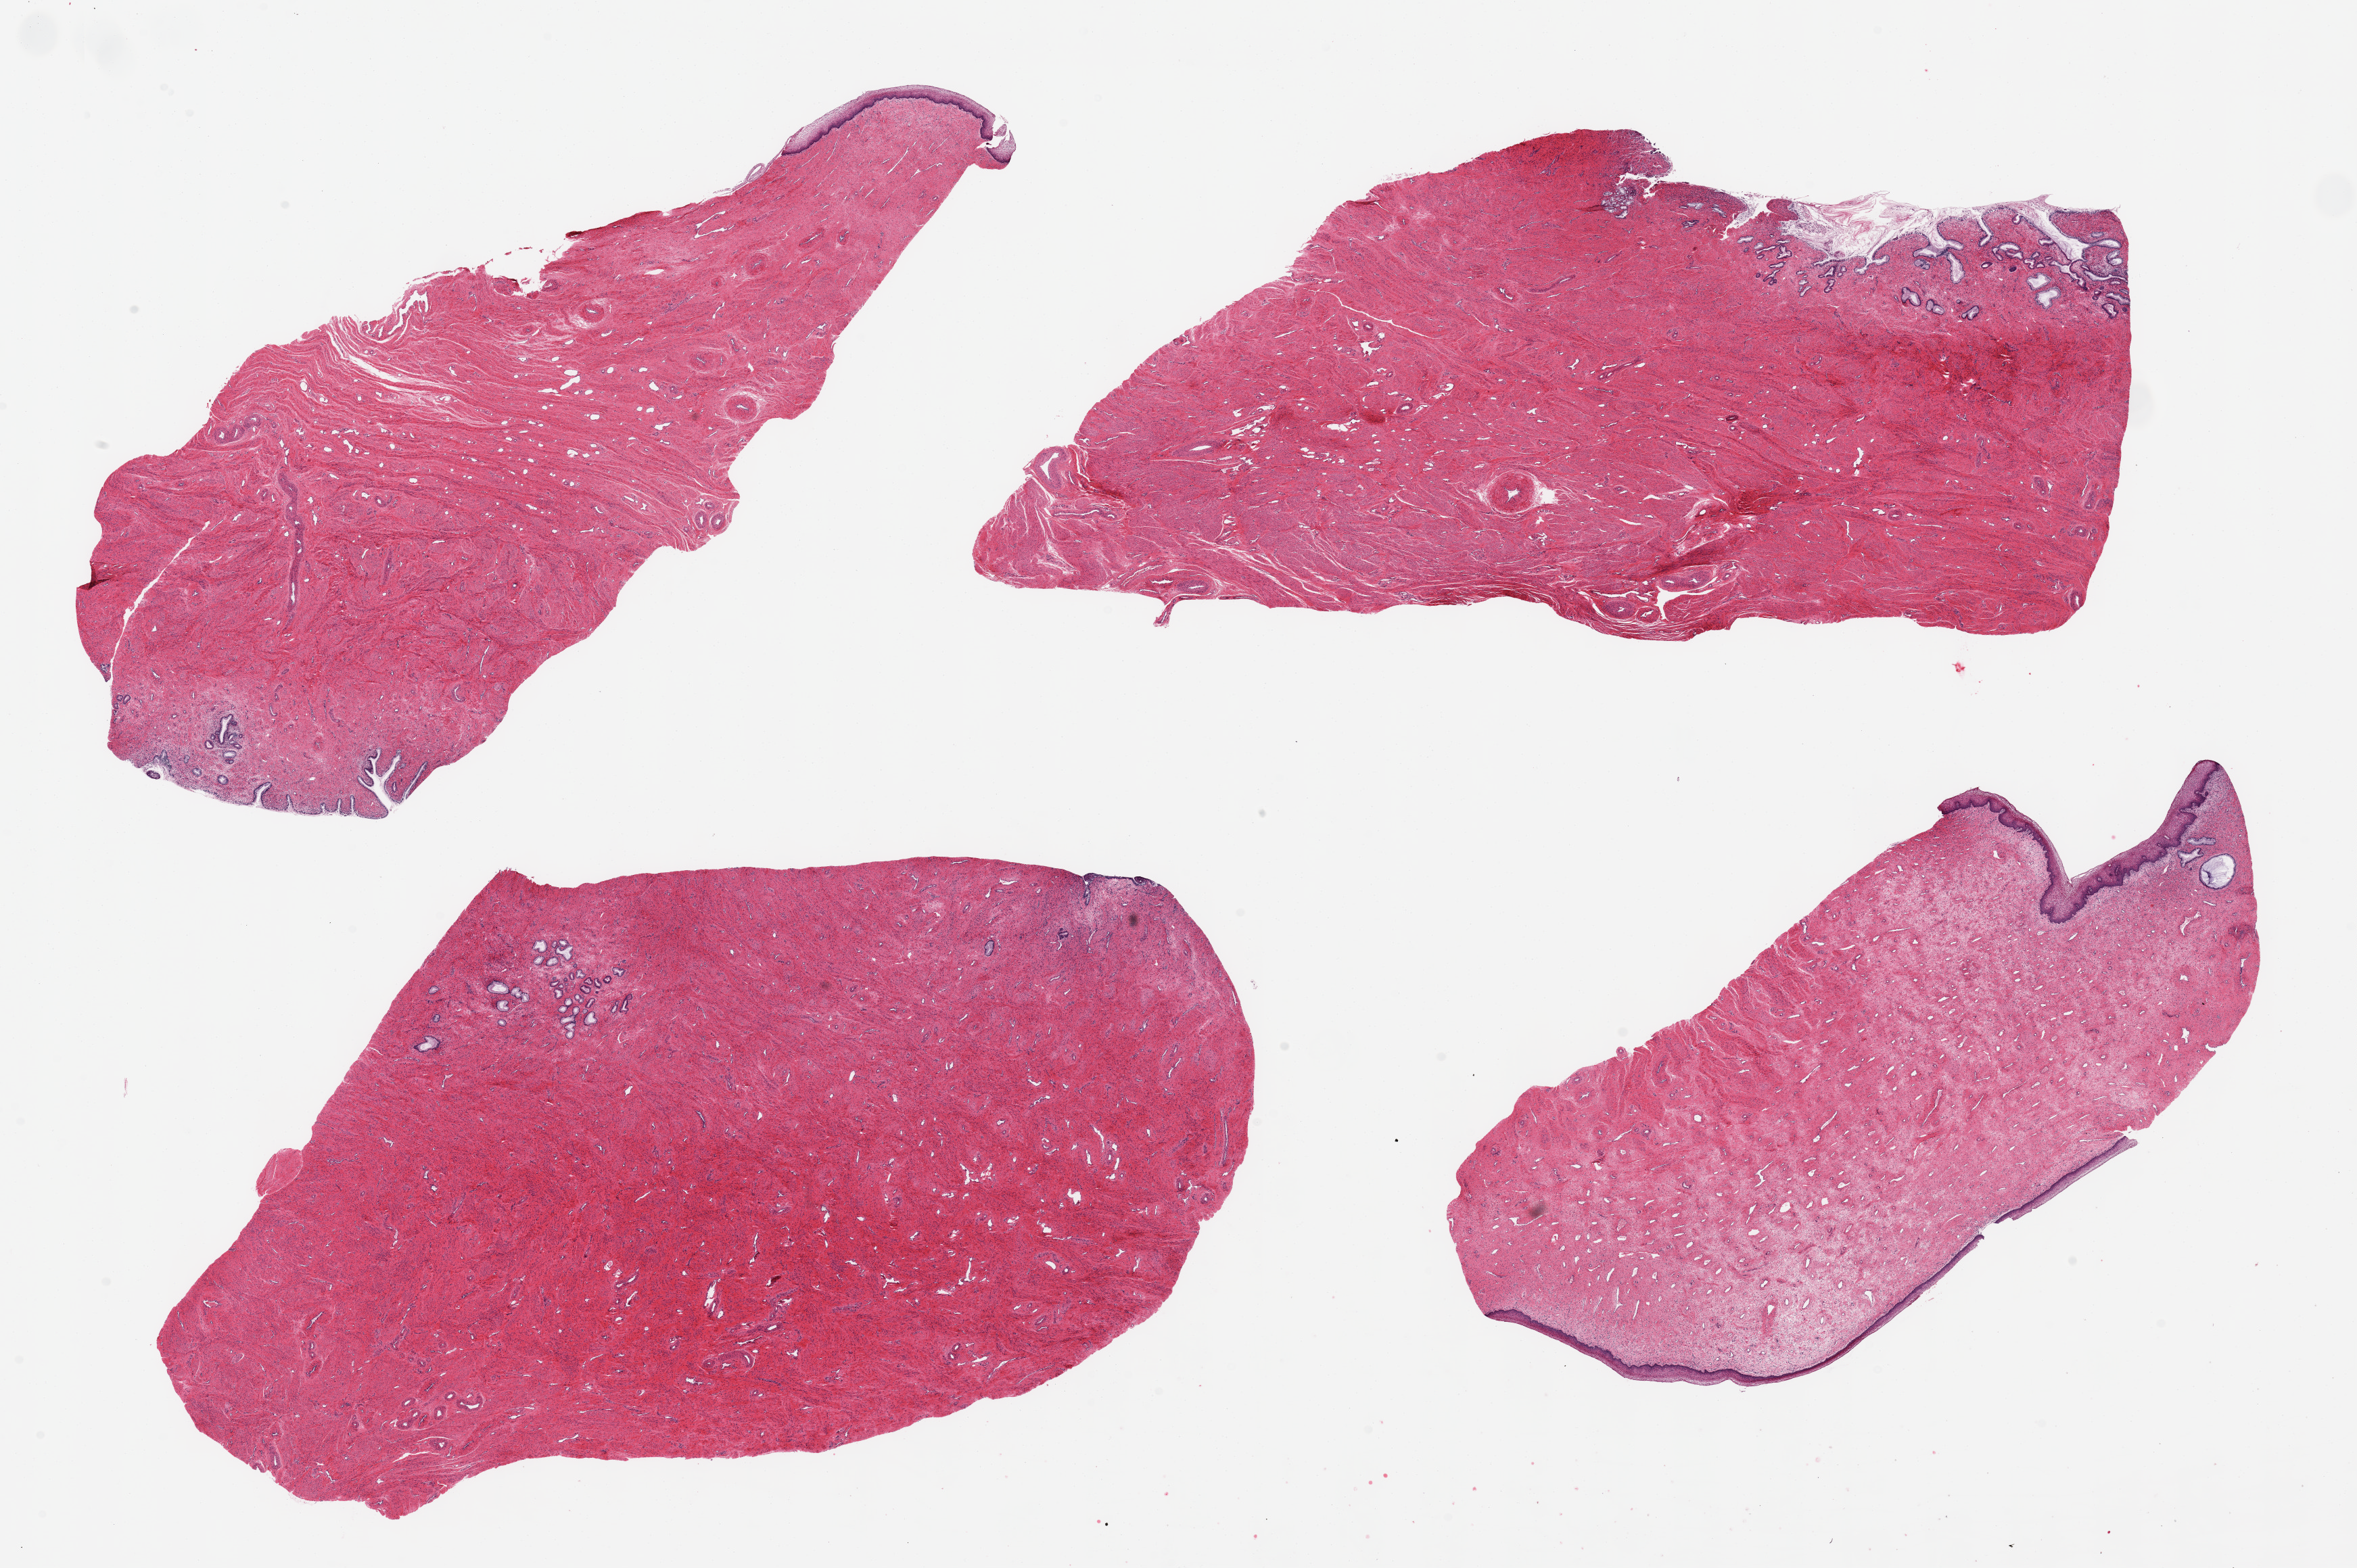
Digitized H&E-stained section — whole scanned area (about 27.6 x 18.3 mm, acquisition: 20x scan) shown as a low-resolution overview, PAXgene-fixed, paraffin-embedded tissue, section of exocervix (target tissue), tissue donor sample. Donor sex: female.
Reviewer comment on this tissue sample: 4 pieces endocervix; 2 are ectocervix, 2 are endocervix.